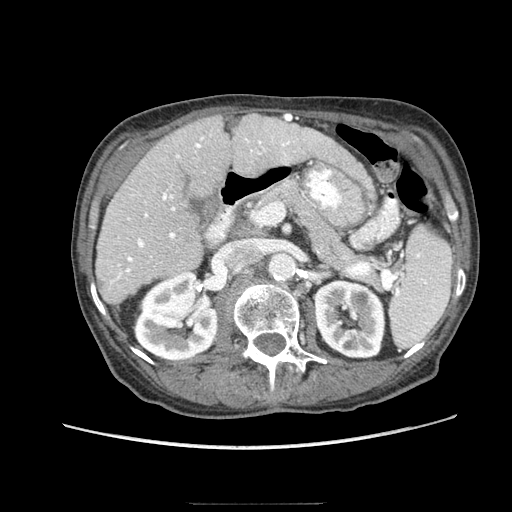
Contrast-enhanced abdominal CT (liver protocol), one axial slice. Position 40 of 83 along the scan axis. Reconstruction kernel STANDARD. 140 kVp. Soft-tissue window (W 400 / L 40 HU). 2.5 mm slice thickness. 512 × 512 image matrix, field of view 360 × 360 mm. From the clinical record (not read from this slice): diagnosis: hepatocellular carcinoma (patient treated with transarterial chemoembolisation; whether this scan precedes or follows treatment is not stated here); TNM stage (as recorded): Stage-I.
Annotated regions visible in this slice (semi-automatic segmentation, software-assisted and operator-edited):
- liver parenchyma outside the tumour (the mass and vessels are separate outlines, so this box may not span the whole liver): bounding box [x1, y1, x2, y2] px = [96, 114, 348, 304]
- liver vessels: [110, 136, 290, 284]